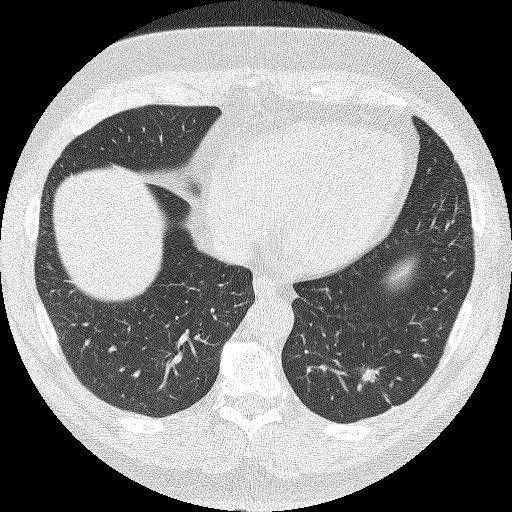
Low-dose screening chest CT, one axial slice. Position 41 of 140 along the scan axis. Lung window (W 1500 / L -600 HU). 2 mm slice thickness. 512 × 512 image matrix.
Structures marked on this image (expert manual segmentation):
- lesion 1 (tumor, lower lobe of left lung): bounding box [x1, y1, x2, y2] px = [362, 368, 381, 383]